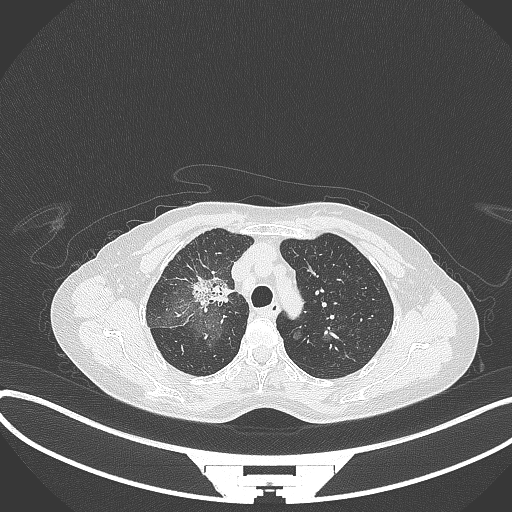
Chest CT, one axial slice; position 241 of 284 along the scan axis; 120 kVp; lung window (W 1500 / L -600 HU); 512 × 512 image matrix, field of view 400 × 400 mm. Female patient, age 59 years. From the clinical record (not read from this slice): clinical TNM (as recorded): T3 N0 M0.
Annotated regions visible in this slice (rectangle marked by the reading radiologist):
- lung tumour (recorded histology: adenocarcinoma): bounding box [x1, y1, x2, y2] px = [190, 274, 233, 310]